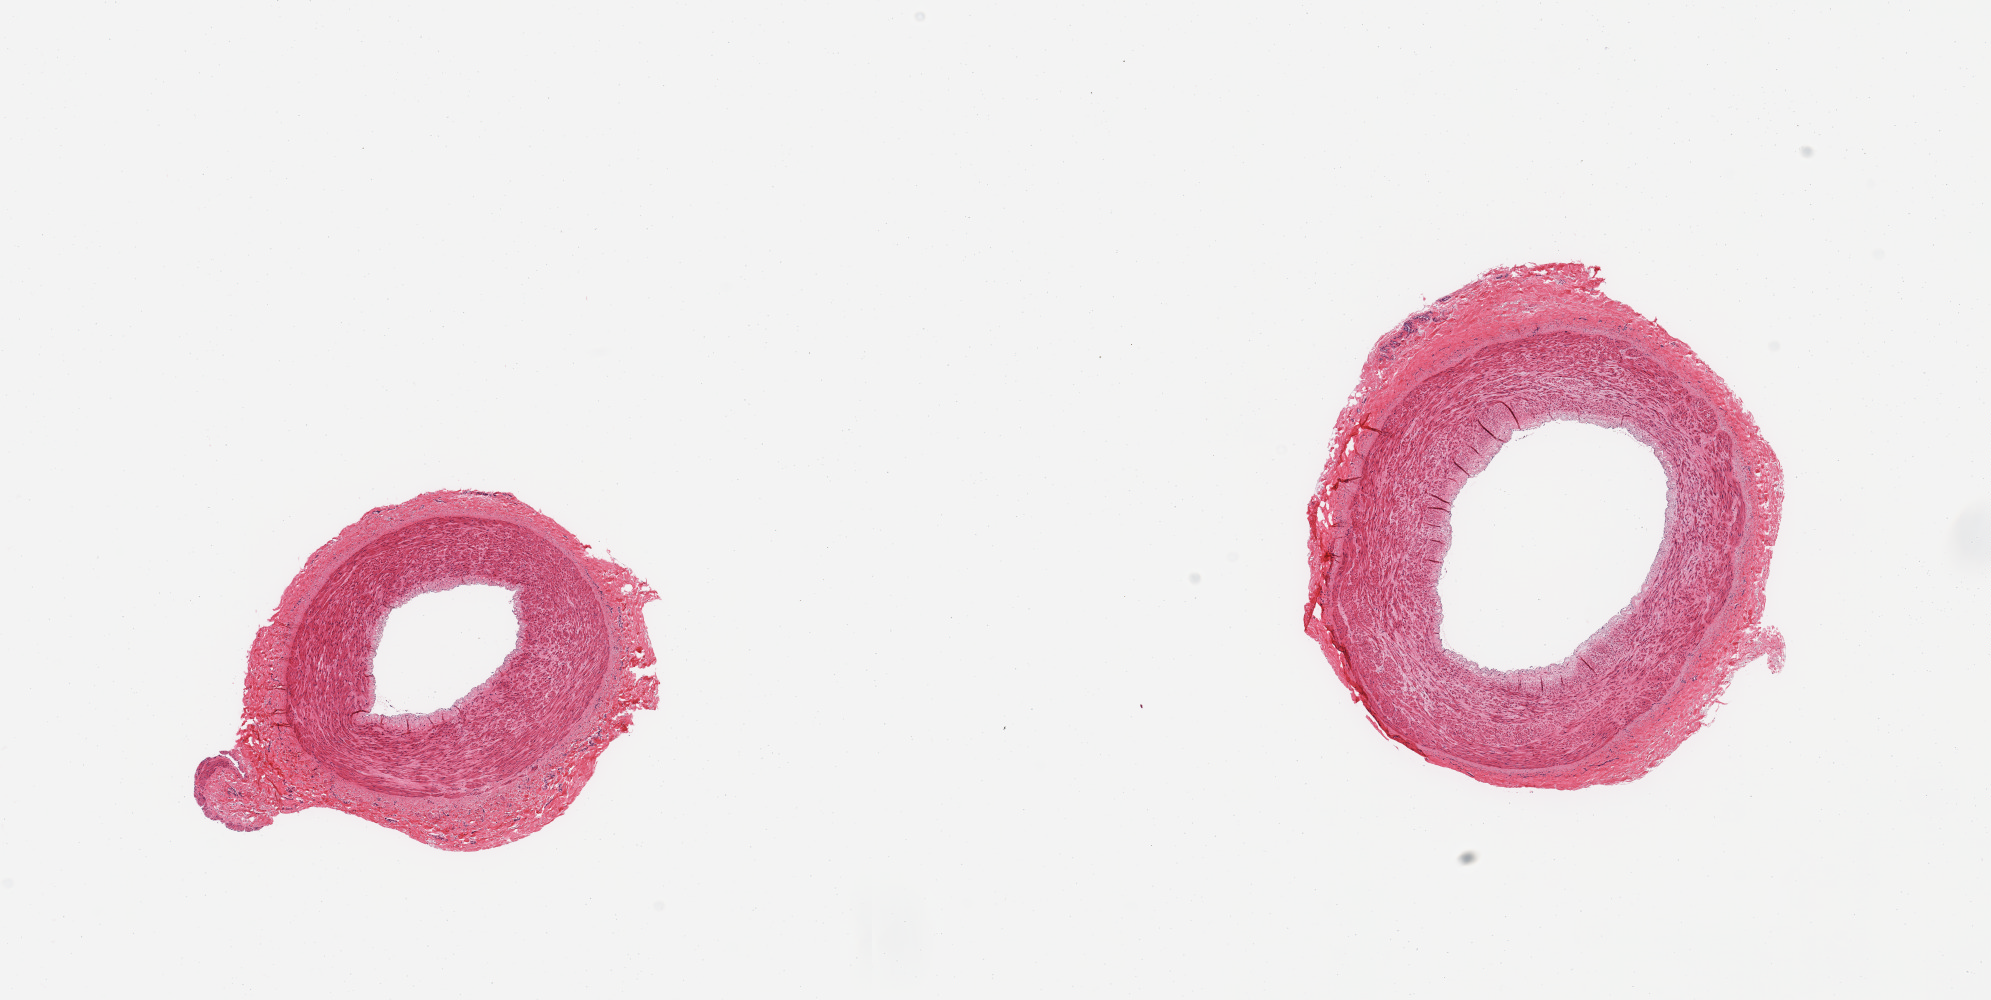
Digitized haematoxylin and eosin-stained section, brightfield — shown as a low-resolution overview of the whole scanned area (about 15.8 x 7.9 mm); PAXgene-fixed, paraffin-embedded tissue; sampled site (target tissue): tibial artery; tissue donor sample.
Reviewer comment on this tissue sample: 2 pieces; patent vessels with attached adventitia, ~1.0mm and 0.5mm; no plaques.